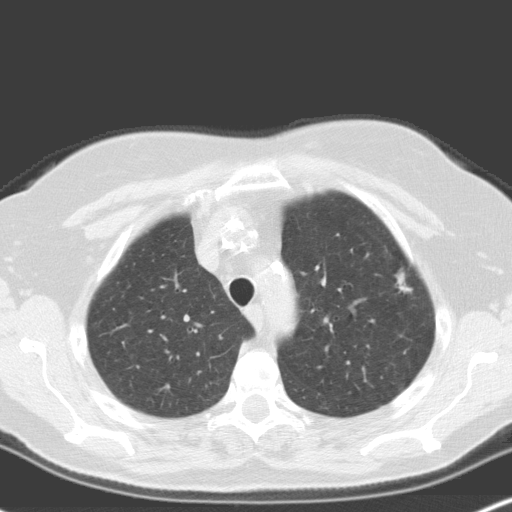
Low-dose screening chest CT, one axial slice. Slice 133 of 160 in the series (ordered by position). Lung window (W 1500 / L -600 HU). 3.2 mm slice thickness. 512 × 512 image matrix.
Outlined on this slice (outlined manually by an expert reader):
- lesion 2 (nodule): box from (x=397, y=273) to (x=410, y=292) px